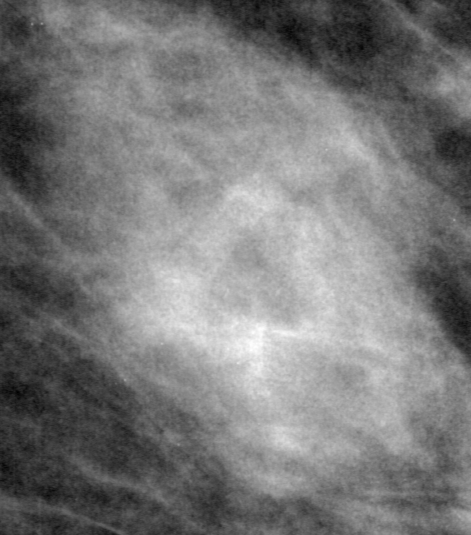
Cropped region of a digitized screen-film mammogram centred on a radiologist-marked abnormality; right breast; MLO view; BI-RADS breast density category 2 (scale 1–4).
- Finding: mass, shape oval, margins ill defined; BI-RADS assessment category 4; subtlety rating 4 on a 1 (subtle) to 5 (obvious) scale; pathology (as recorded): benign.